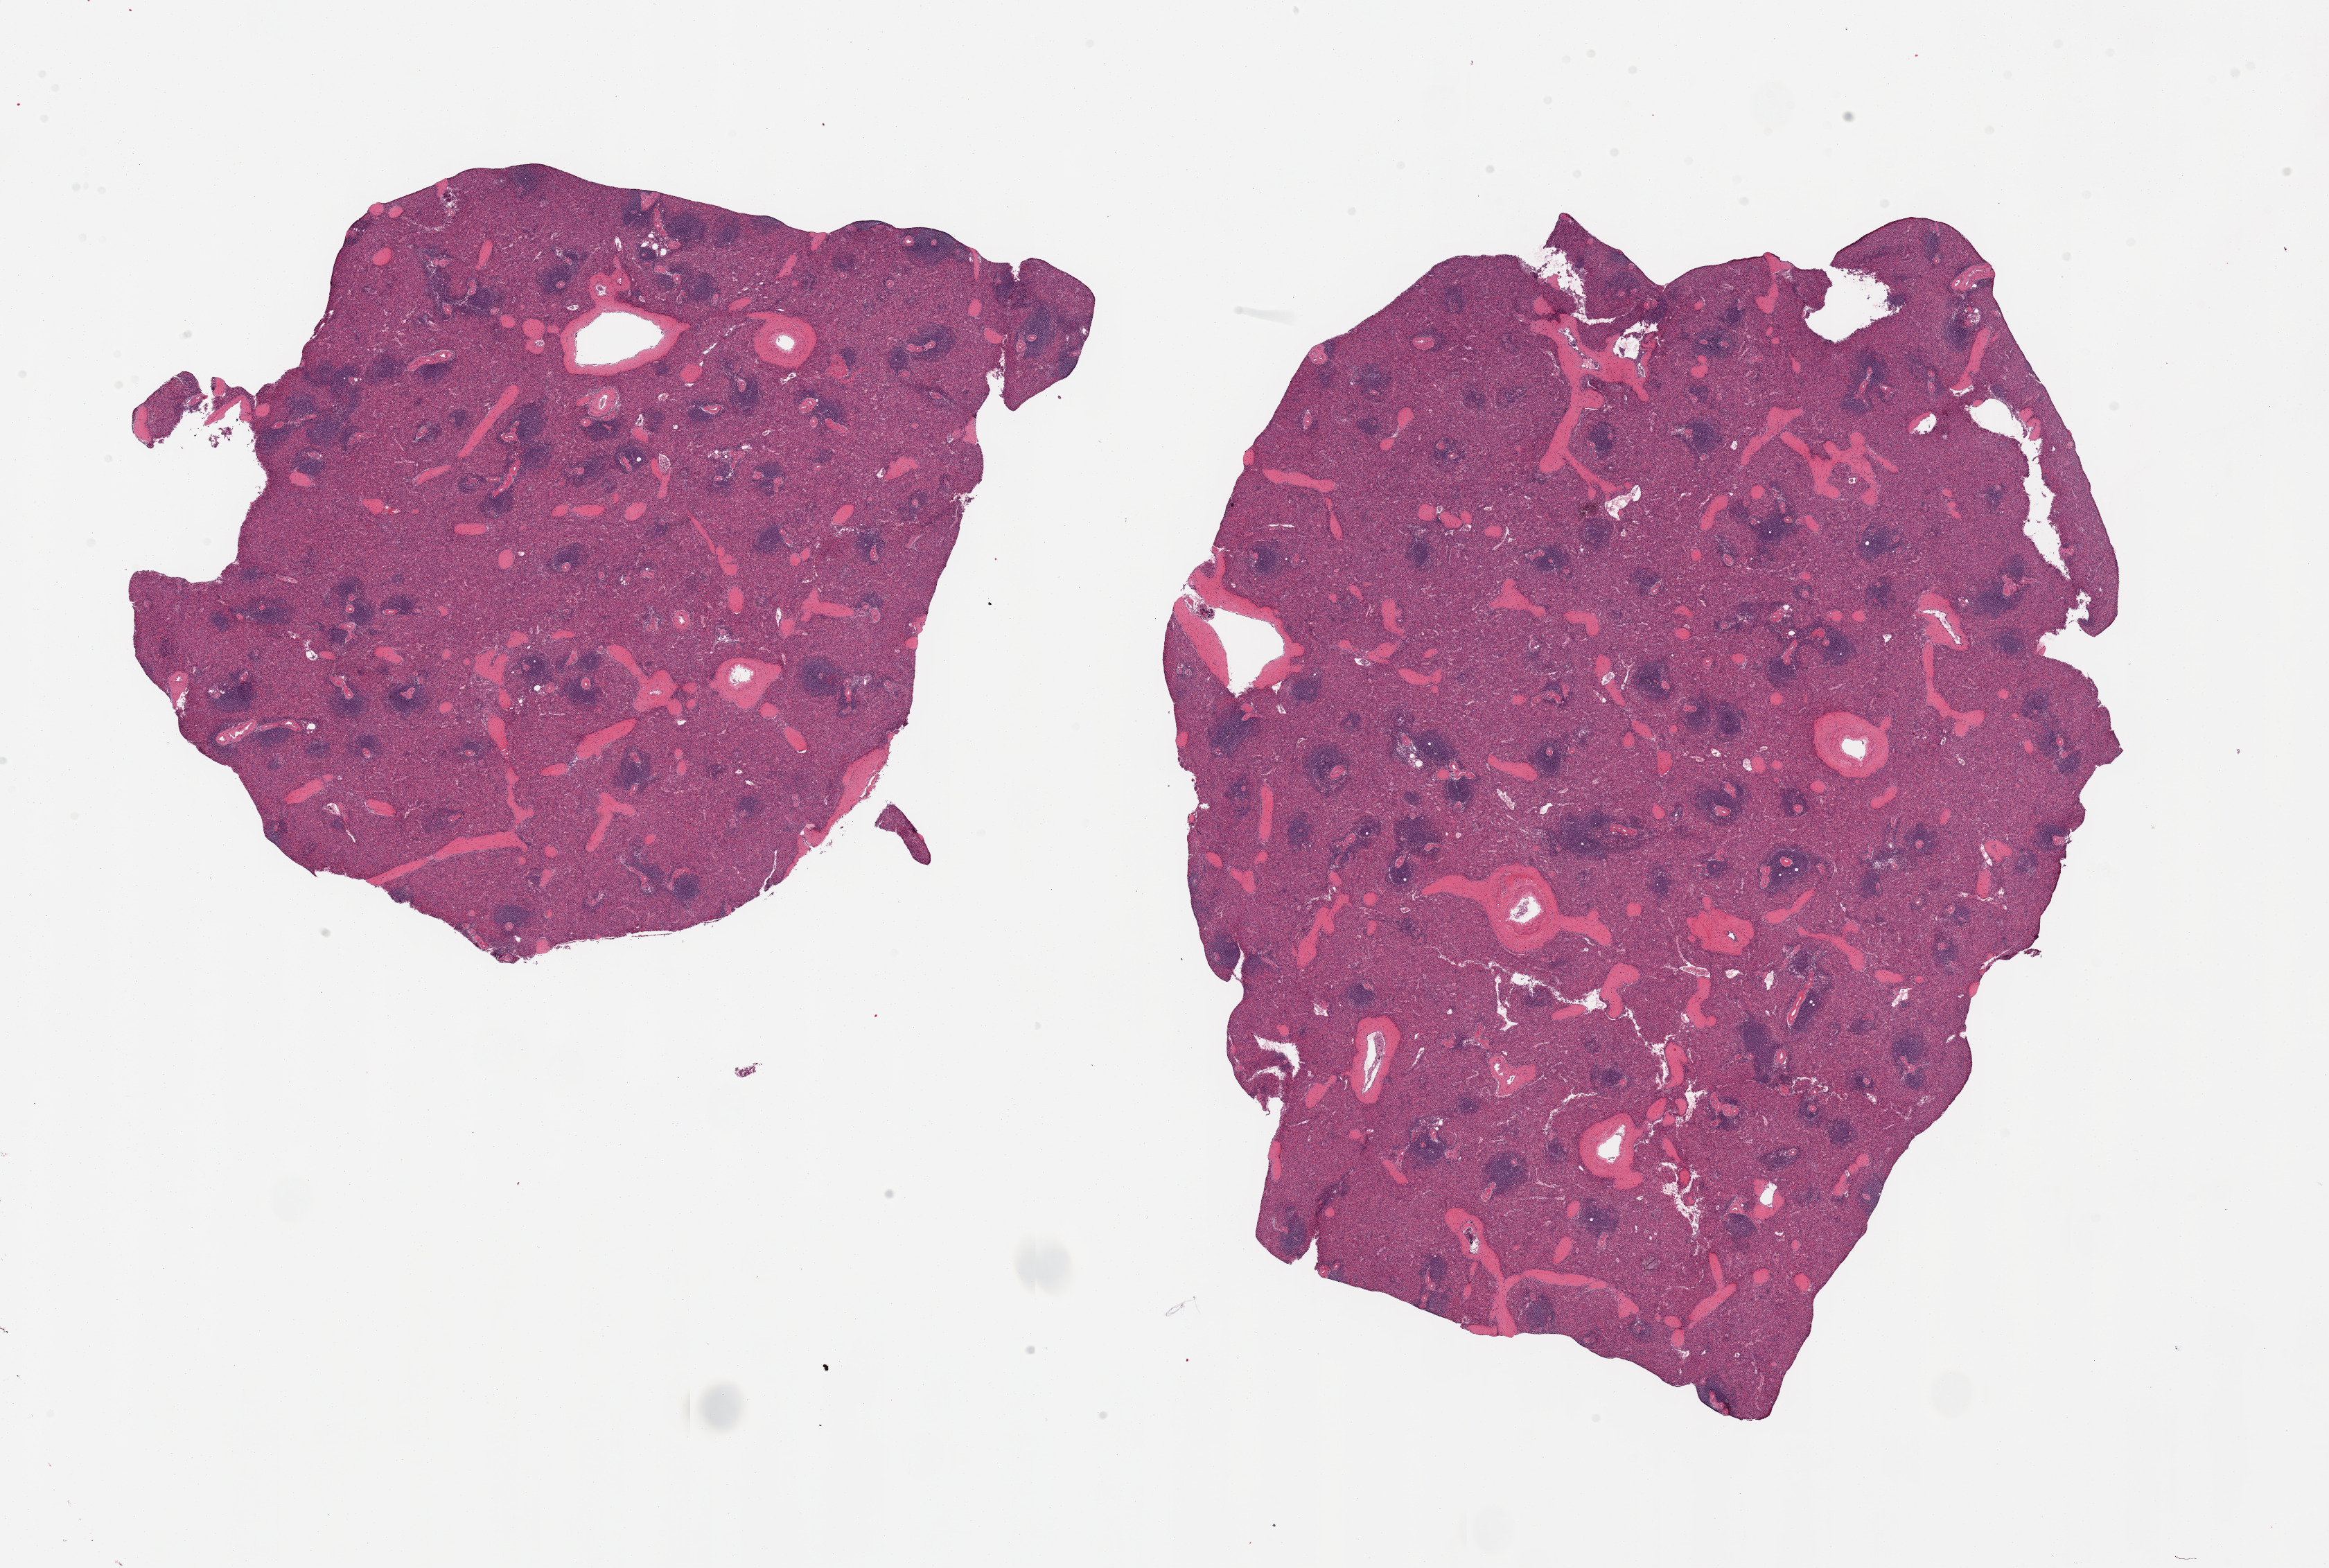
Digitized hematoxylin and eosin (H&E)-stained section, whole scanned area (about 26.6 x 17.9 mm, slide scanned at 20x) shown as a low-resolution overview, PAXgene-fixed, paraffin-embedded tissue, sampled site (target tissue): spleen, tissue donor sample.
* pathologist's review note for this sample: 2 pieces; oversized, few vessels with ? fibrinoid necrosis